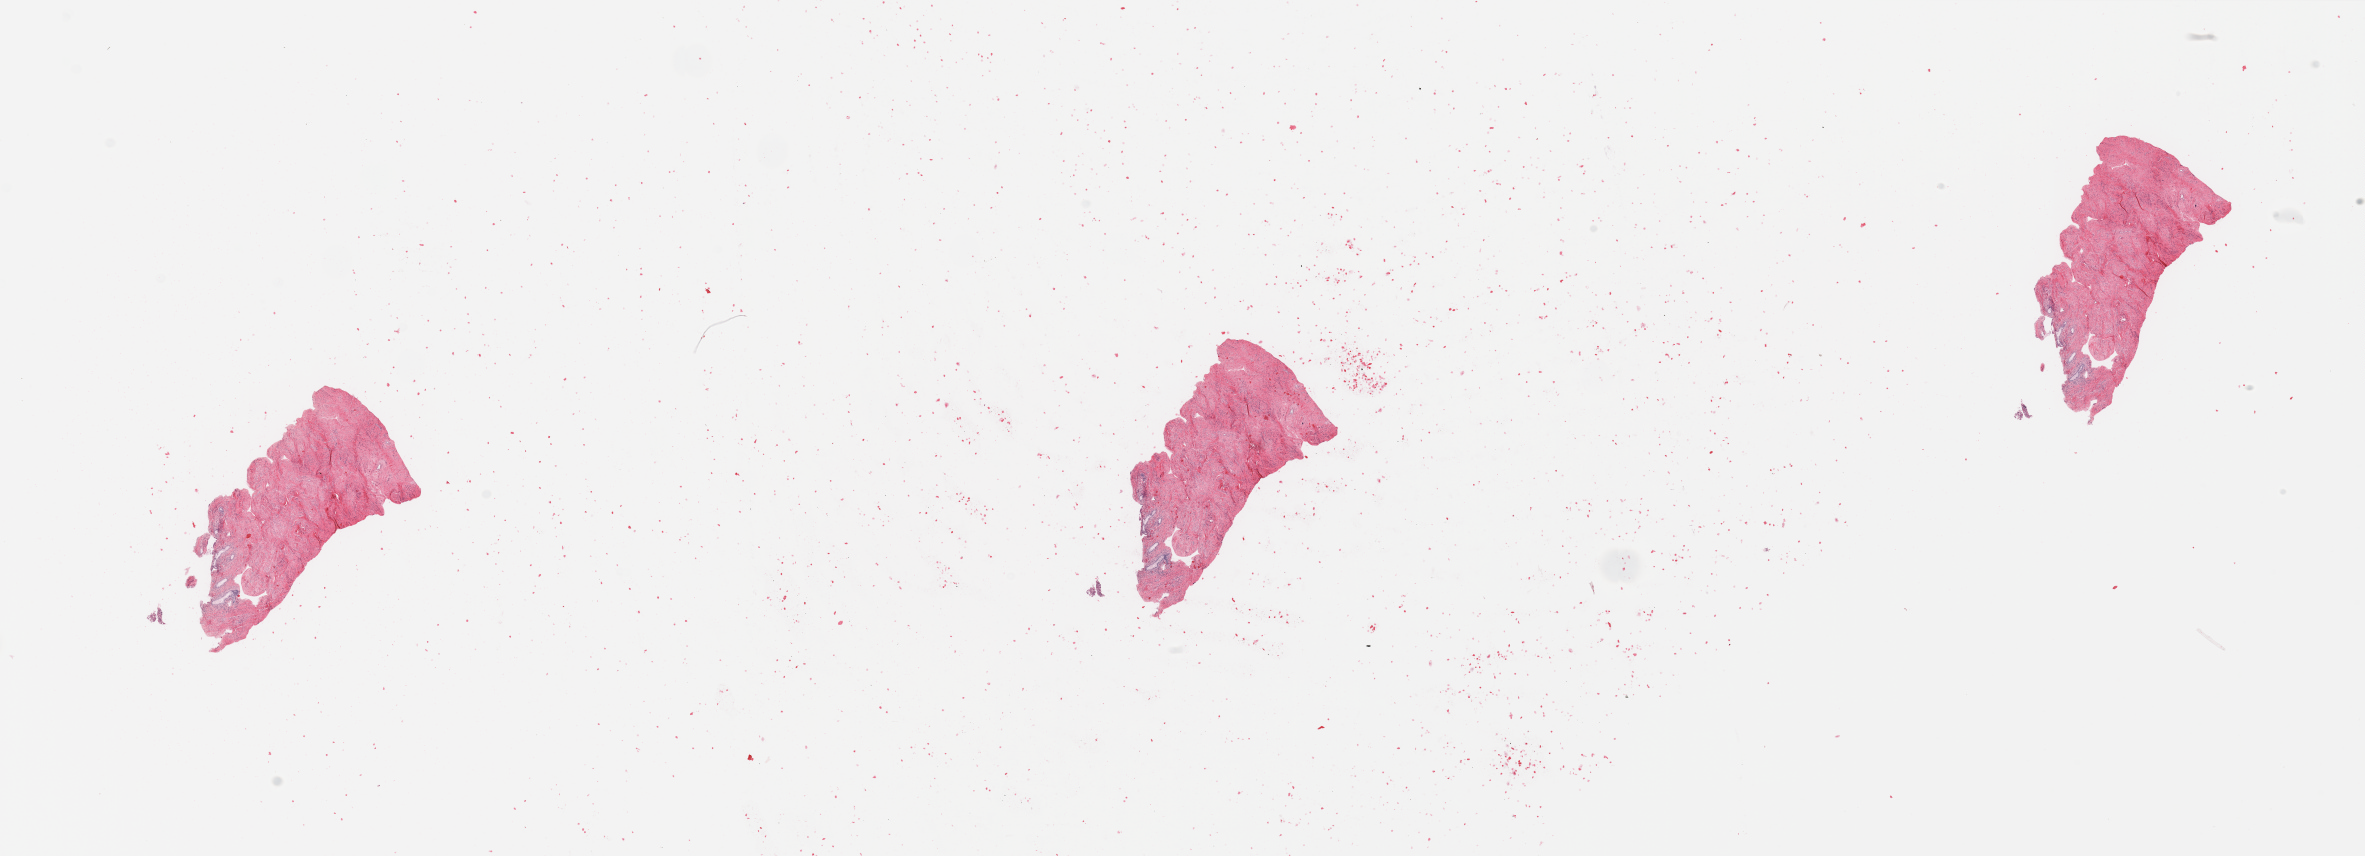
Whole-slide histology image, H&E, shown as a low-resolution overview of the whole scanned area (about 37.4 x 13.5 mm, from a 20x scan); normal (non-tumour) tissue sample, uterus. Patient: female, age 86 years.
• this section: normal (non-tumour) tissue from the same patient
• patient diagnosis: Endometrioid adenocarcinoma, NOS